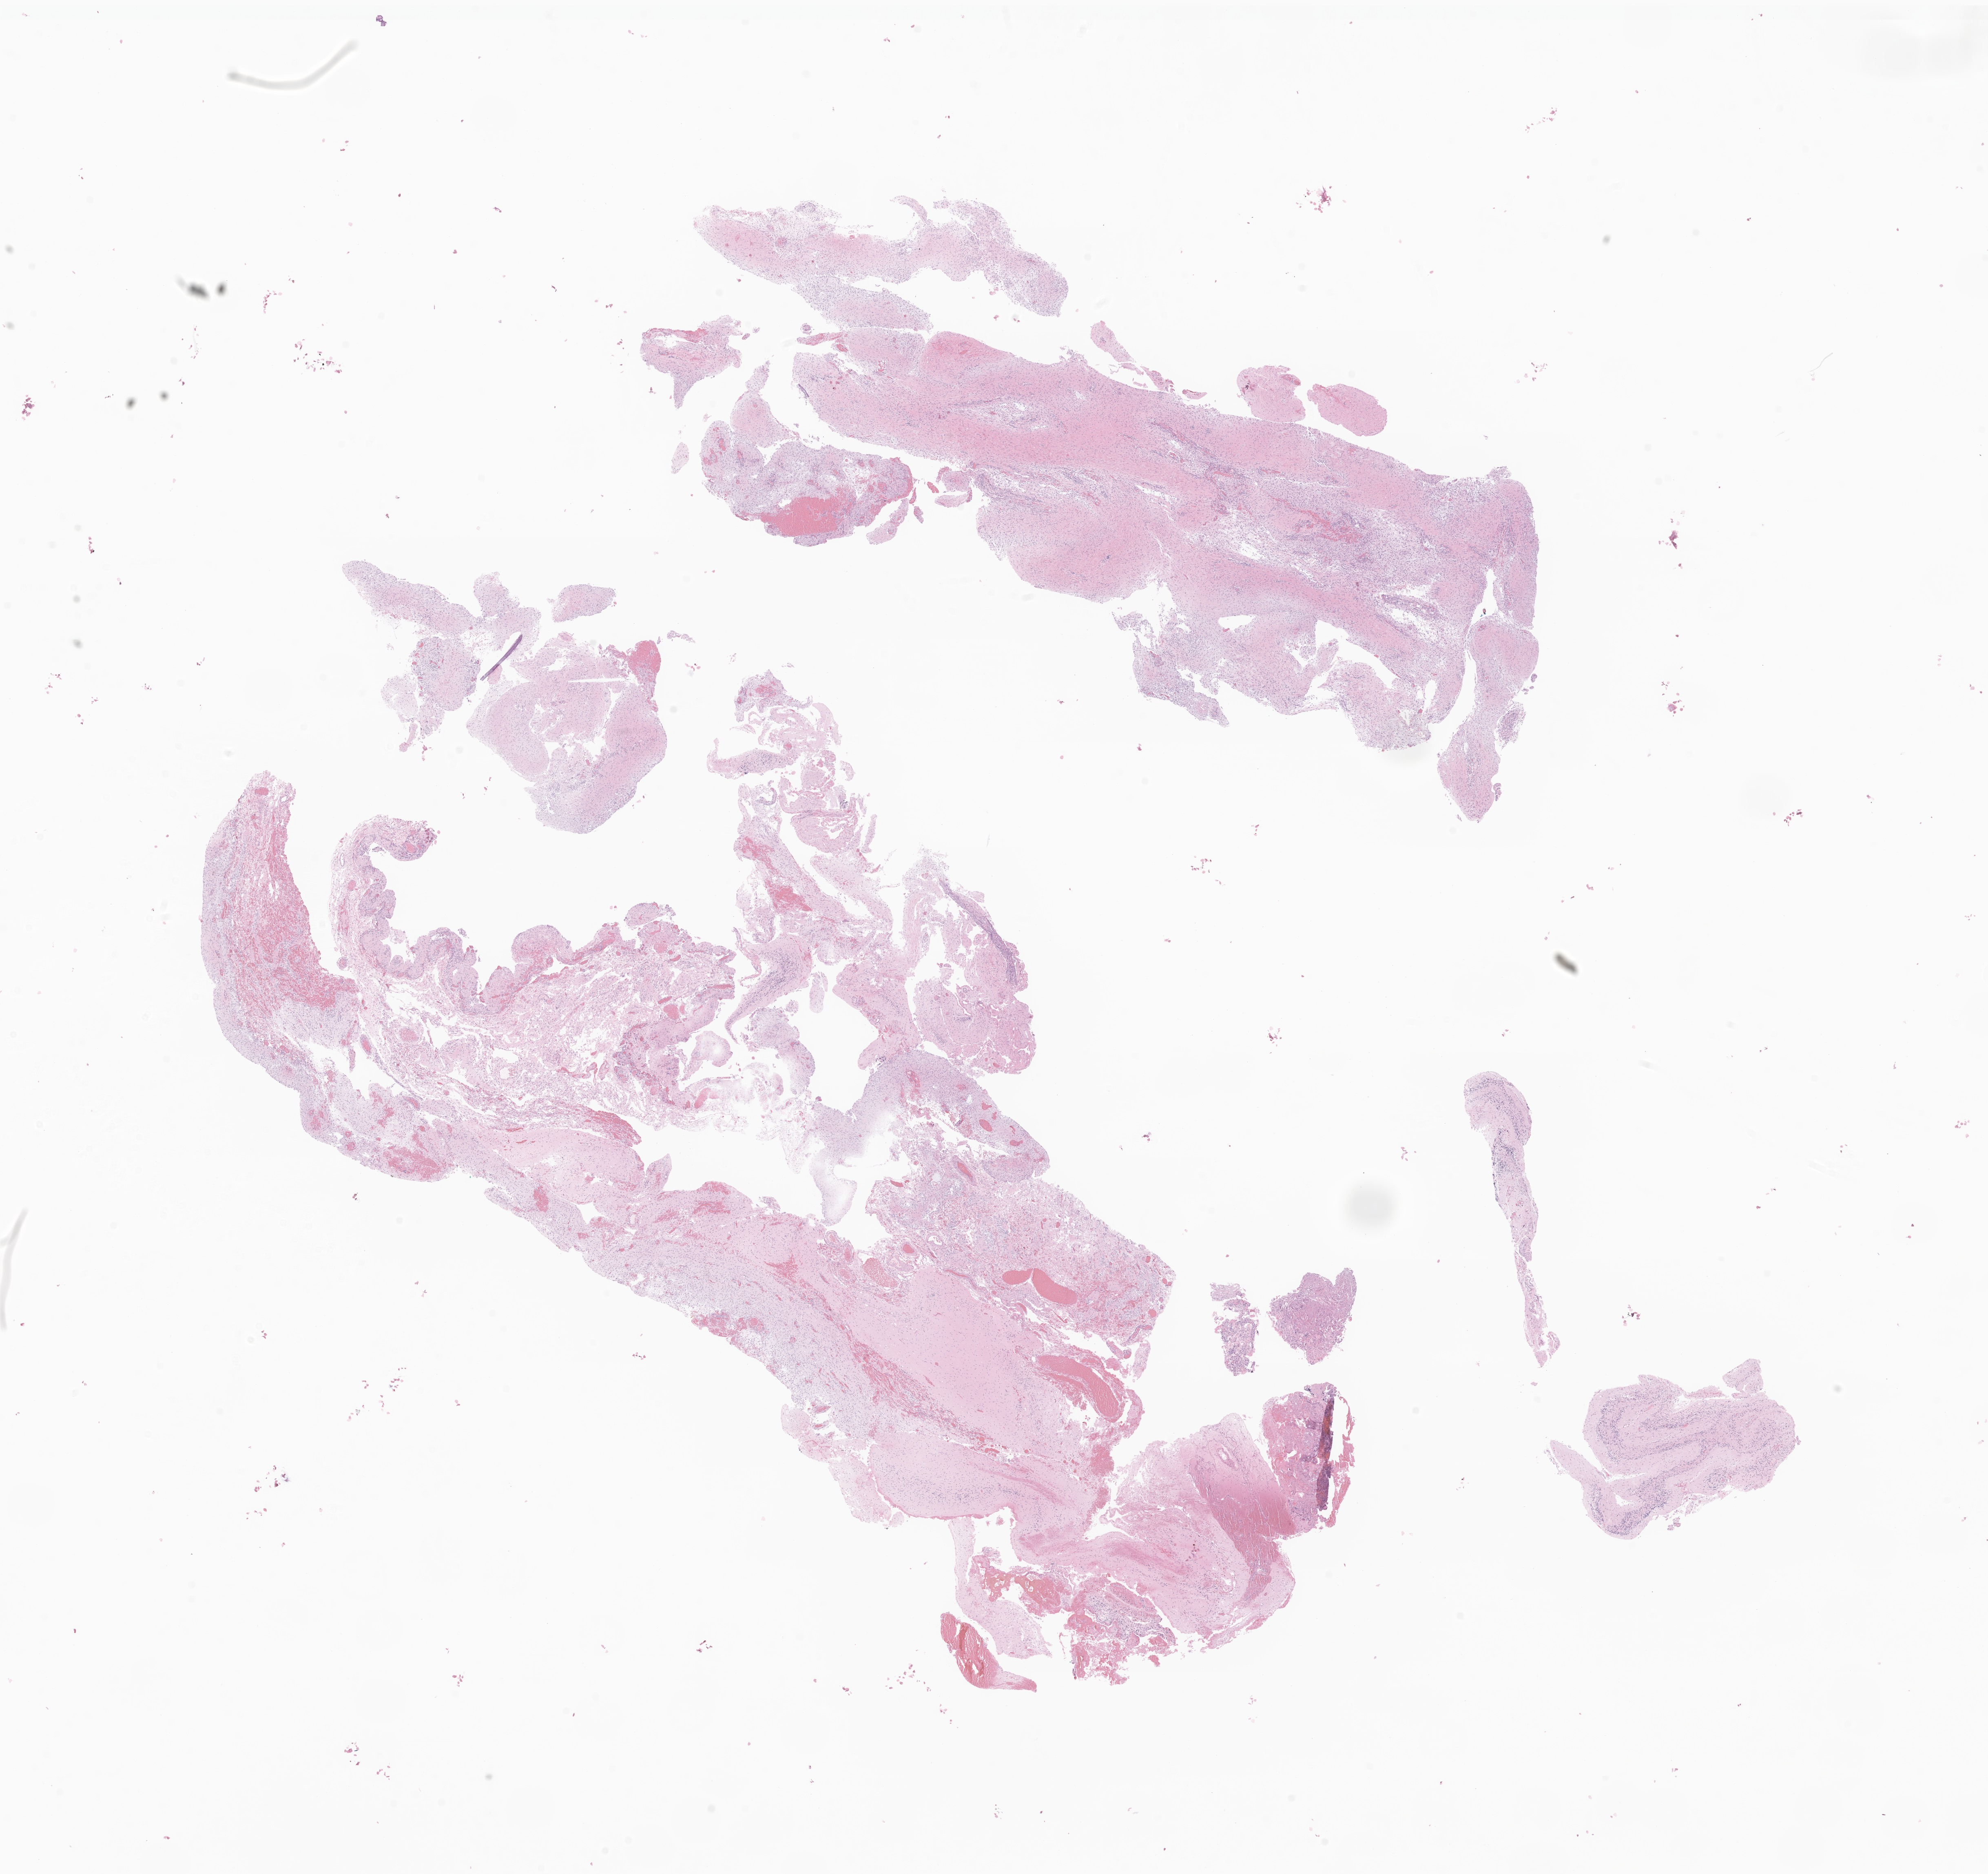
Whole-slide image, haematoxylin and eosin stain of tumor tissue from the brain, shown as a low-resolution overview of the whole scanned area (about 20.5 x 19.4 mm). Formalin-fixed paraffin-embedded section. Patient: male, age 41 months (3 years 5 months).
Diagnosis: Pilocytic astrocytoma.